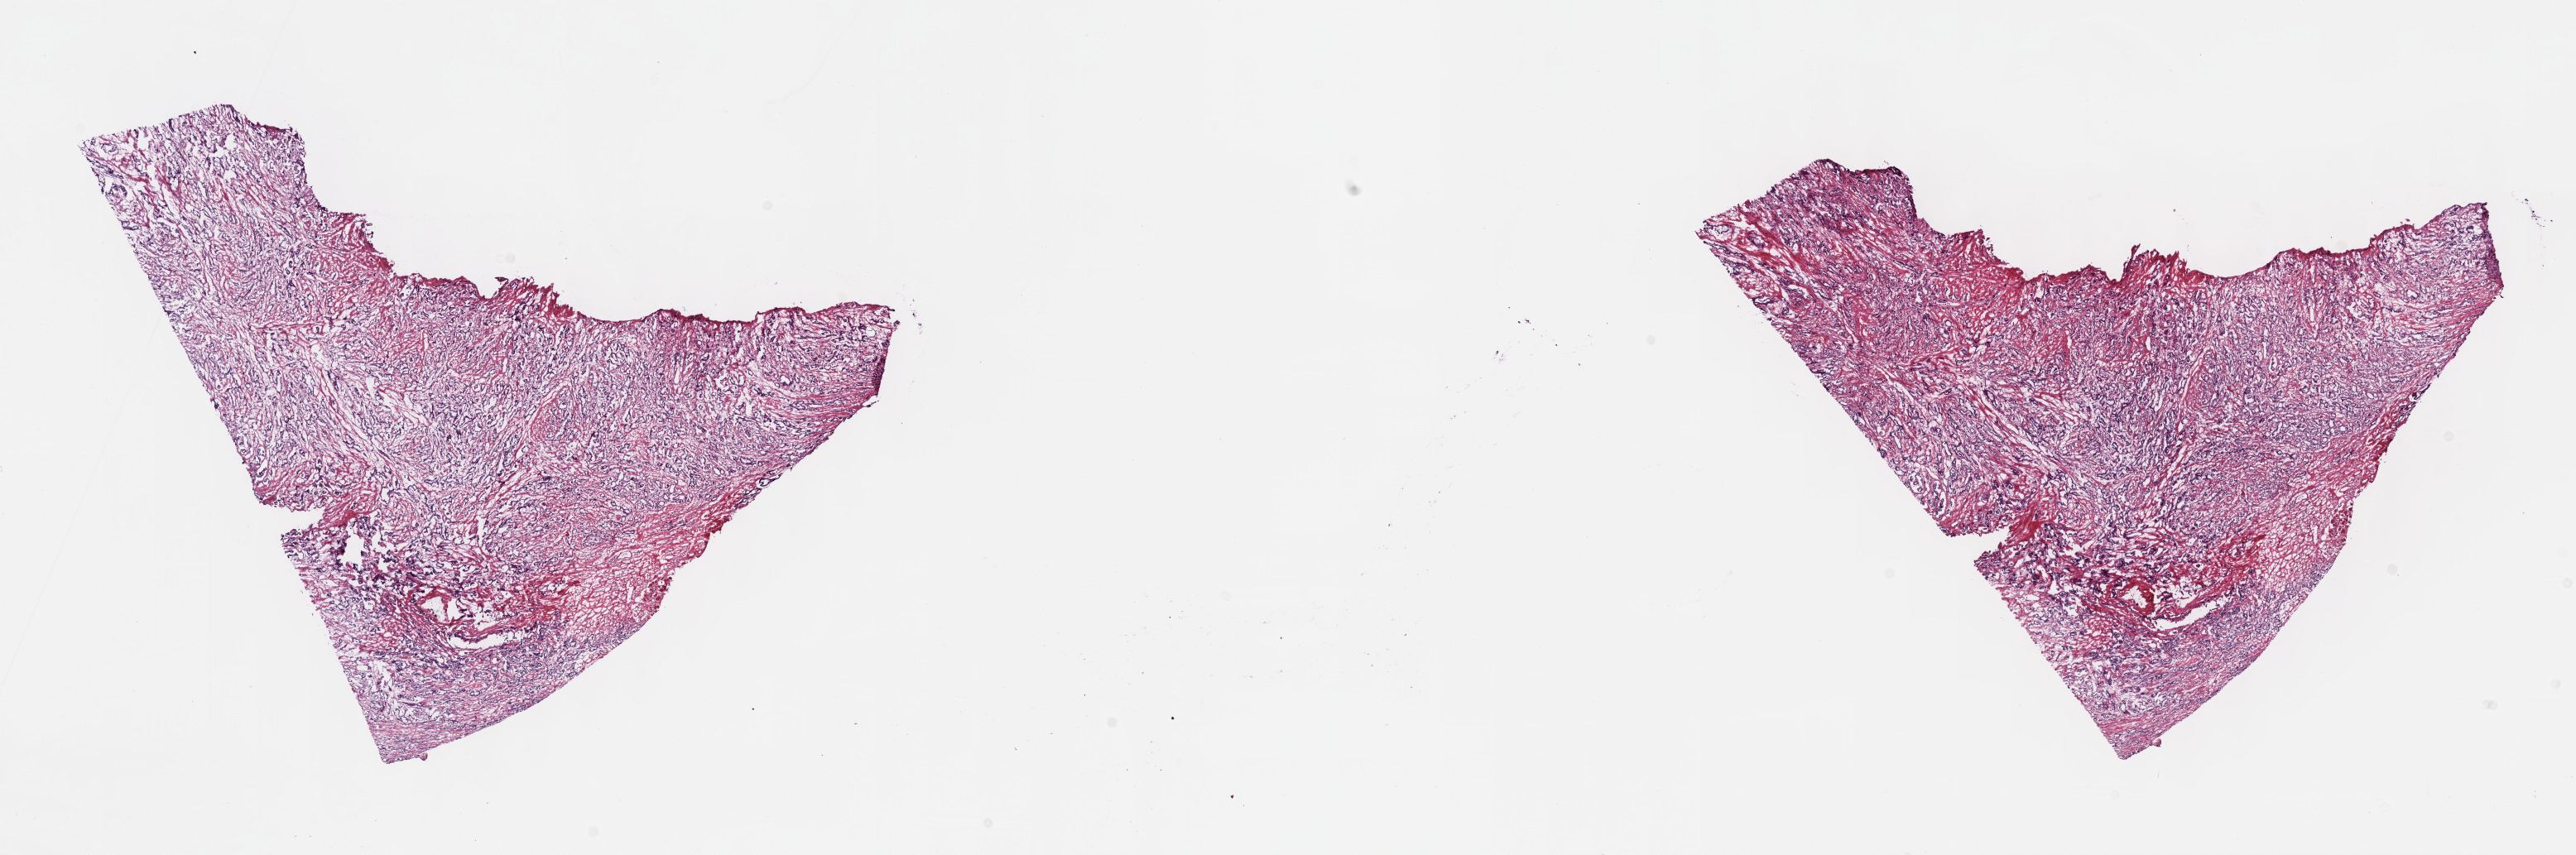
H&E-stained whole-slide image — low-resolution overview of the scanned area, about 25.2 x 8.4 mm (from a 40x scan), frozen section from the top of the tissue portion, prostate, primary tumour sample. Male patient; age at initial diagnosis 60 years.
Diagnosis: Adenocarcinoma, NOS (prostate gland).